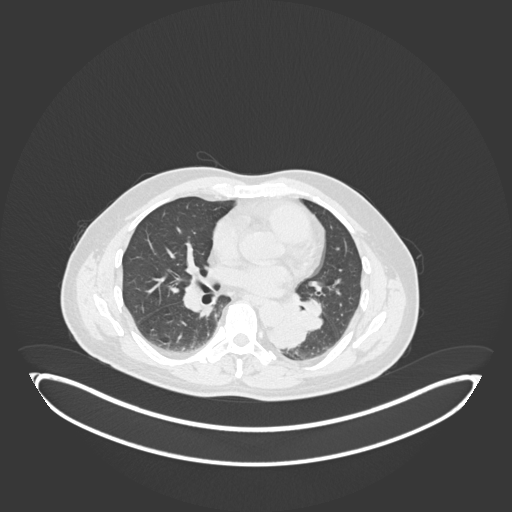
Chest CT, one axial slice. Slice 94 of 258 in the series (ordered by position). Lung window (W 1500 / L -600 HU). 1 mm slice thickness. 512 × 512 image matrix. Patient: male, 54 years. From the clinical record (not read from this slice): clinical TNM (as recorded): T3 N0 M0.
Outlined on this slice (bounding box drawn by a radiologist):
- lung tumour (recorded histology: squamous cell carcinoma): box from (x=262, y=296) to (x=309, y=350) px